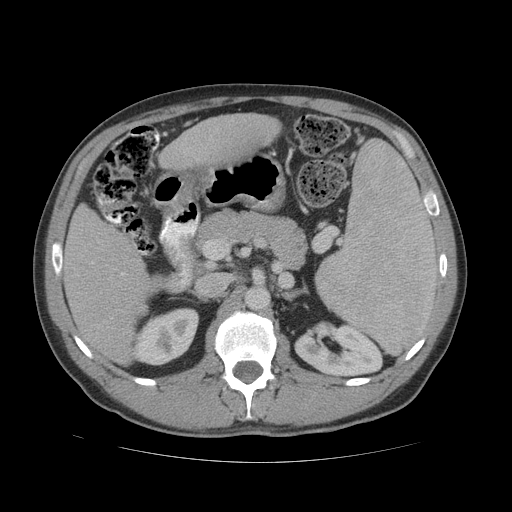
Contrast-enhanced abdominal CT (liver protocol), one axial slice. Slice 26 of 81 in the series (ordered by position). Reconstruction kernel STANDARD. 140 kVp. Soft-tissue window (W 400 / L 40 HU). 2.5 mm slice thickness. 512 × 512 image matrix, field of view 400 × 400 mm. Case-level facts recorded for this patient, not image findings: diagnosis: hepatocellular carcinoma (patient treated with transarterial chemoembolisation; whether this scan precedes or follows treatment is not stated here); TNM stage (as recorded): Stage-IVB; Child-Pugh class: B; tumour nodularity: multinodular.
Annotated regions visible in this slice (semi-automatically segmented with operator editing):
- liver parenchyma outside the tumour (the mass and vessels are separate outlines, so this box may not span the whole liver): bounding box <60,114,280,364> (left, top, right, bottom; pixels)
- liver vessels: <60,260,124,275>